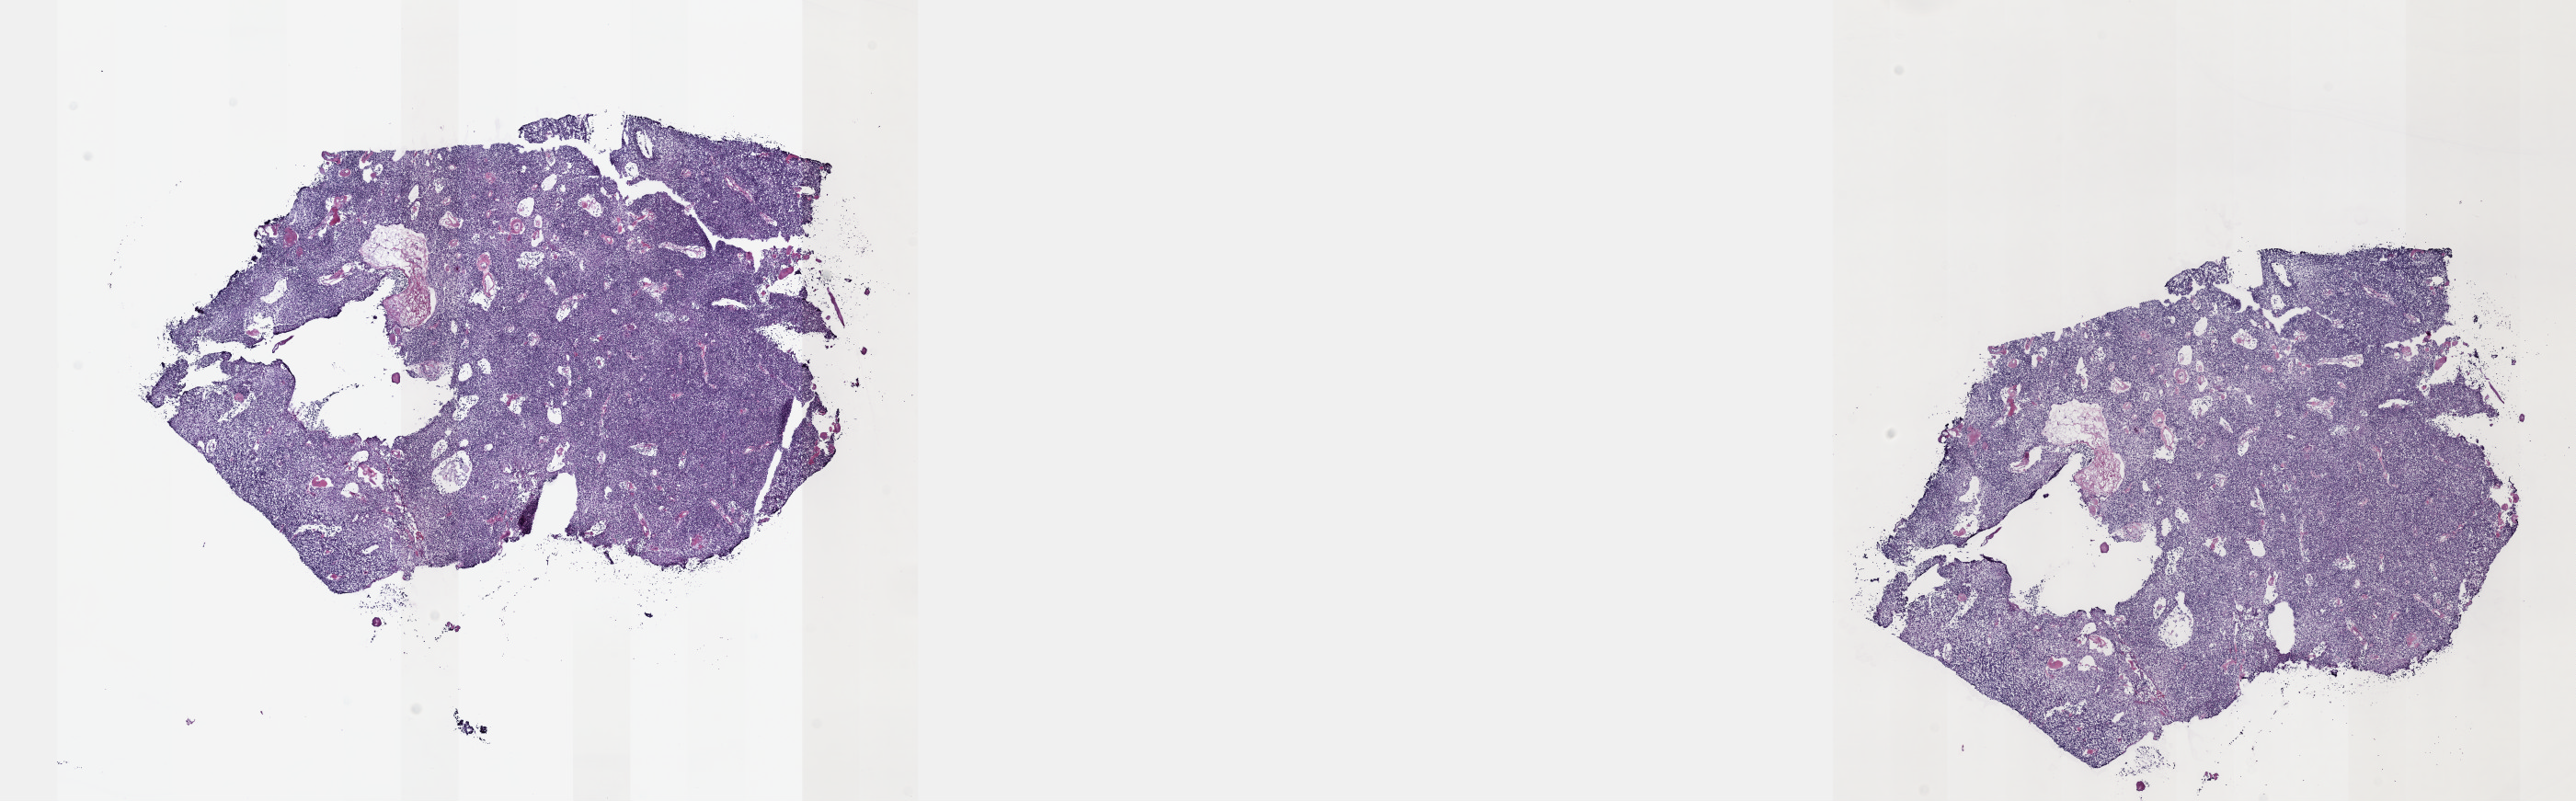
H&E-stained whole-slide image, whole scanned area (about 22.6 x 7.0 mm, slide scanned at 40x) shown as a low-resolution overview, frozen section, primary tumour sample from the thymus. Male, age 42 years at initial diagnosis. Pathologist review of this section (percent, as recorded): tumour cells 99%, tumour nuclei 95%, normal cells 0%, stromal cells 1%, necrosis 0%. Inflammatory infiltration, as recorded: lymphocyte infiltration 0%, monocyte infiltration 0%, neutrophil infiltration 0%.
Histologic diagnosis: Thymoma, type B2, malignant (anterior mediastinum).